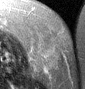
MRI of an extremity soft-tissue mass, one axial slice. Slice 13 of 46 in the series (ordered by position). T2-weighted fat-saturated. MR volume resampled by the dataset authors to the PET/CT grid (not the native acquisition matrix). 3.27 mm slice thickness. 85 × 89 image matrix, field of view 83 × 87 mm. Female patient. From the clinical record (not read from this slice): histological type: leiomyosarcoma; grade: intermediate; site of the primary tumour: parascapusular.
Structures marked on this image (expert contour drawn on MRI and transferred to this co-registered scan by the dataset authors):
- gross tumour volume including surrounding oedema: bounding box <31,34,64,74> (left, top, right, bottom; pixels)
- gross tumour volume (mass): <31,46,64,72>